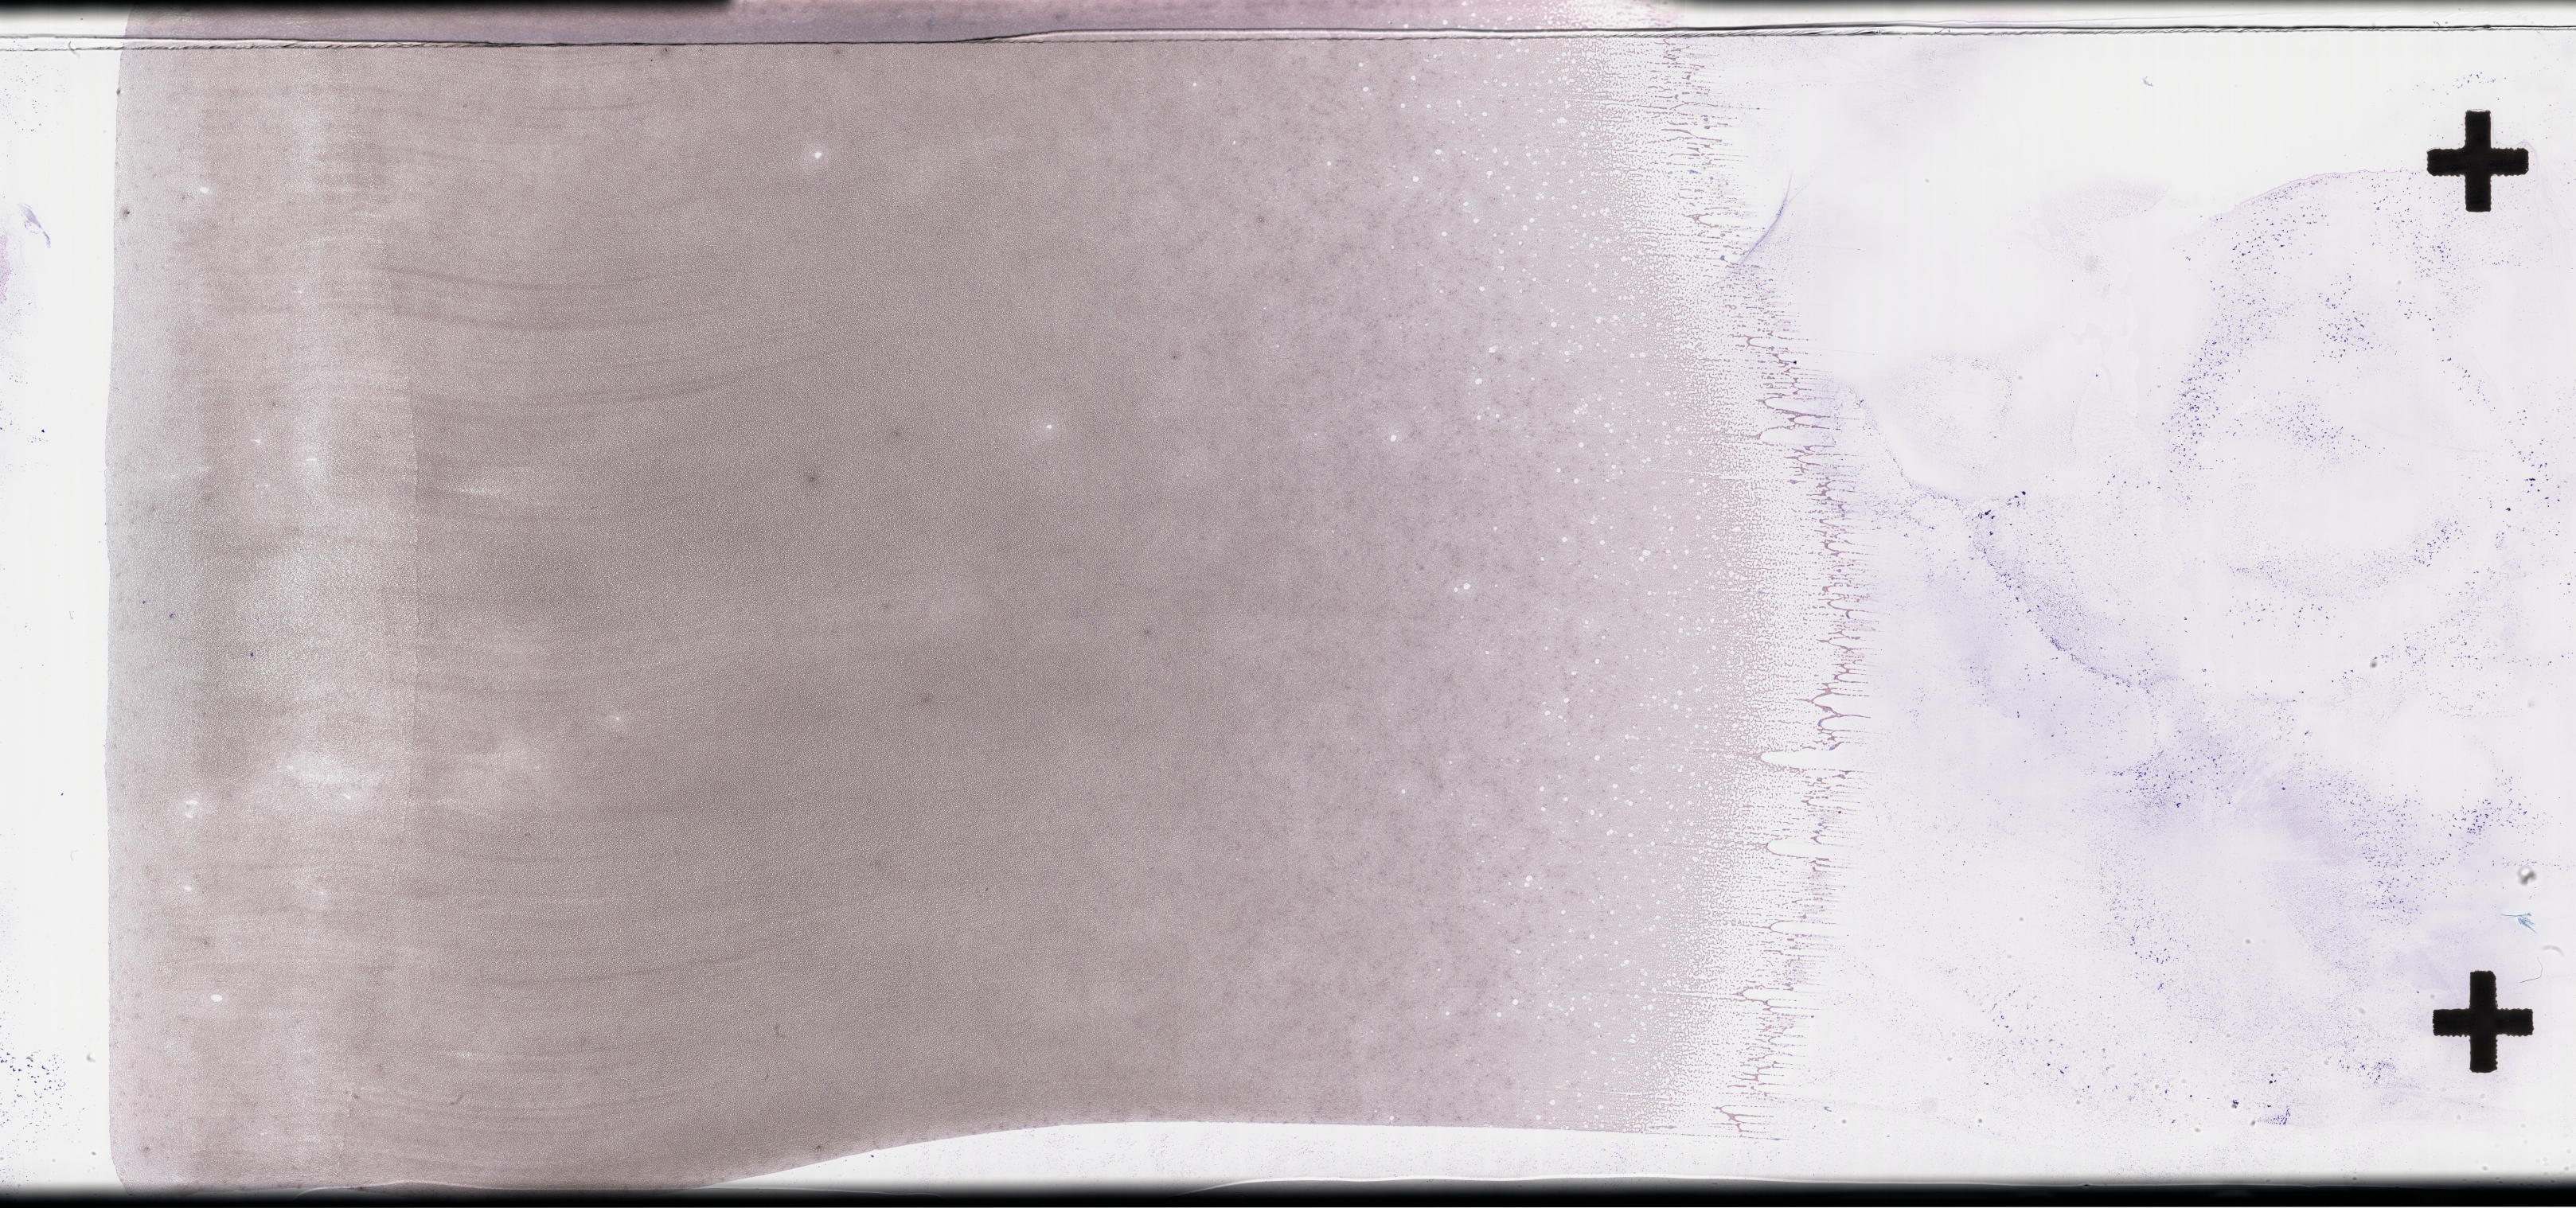
Wright–Giemsa-stained whole blood smear, whole-slide image — a low-resolution overview of the entire scanned area, about 52.3 x 24.5 mm; specimen time point: collected on treatment. Patient: male.
From a patient with: Plasma Cell Myeloma.